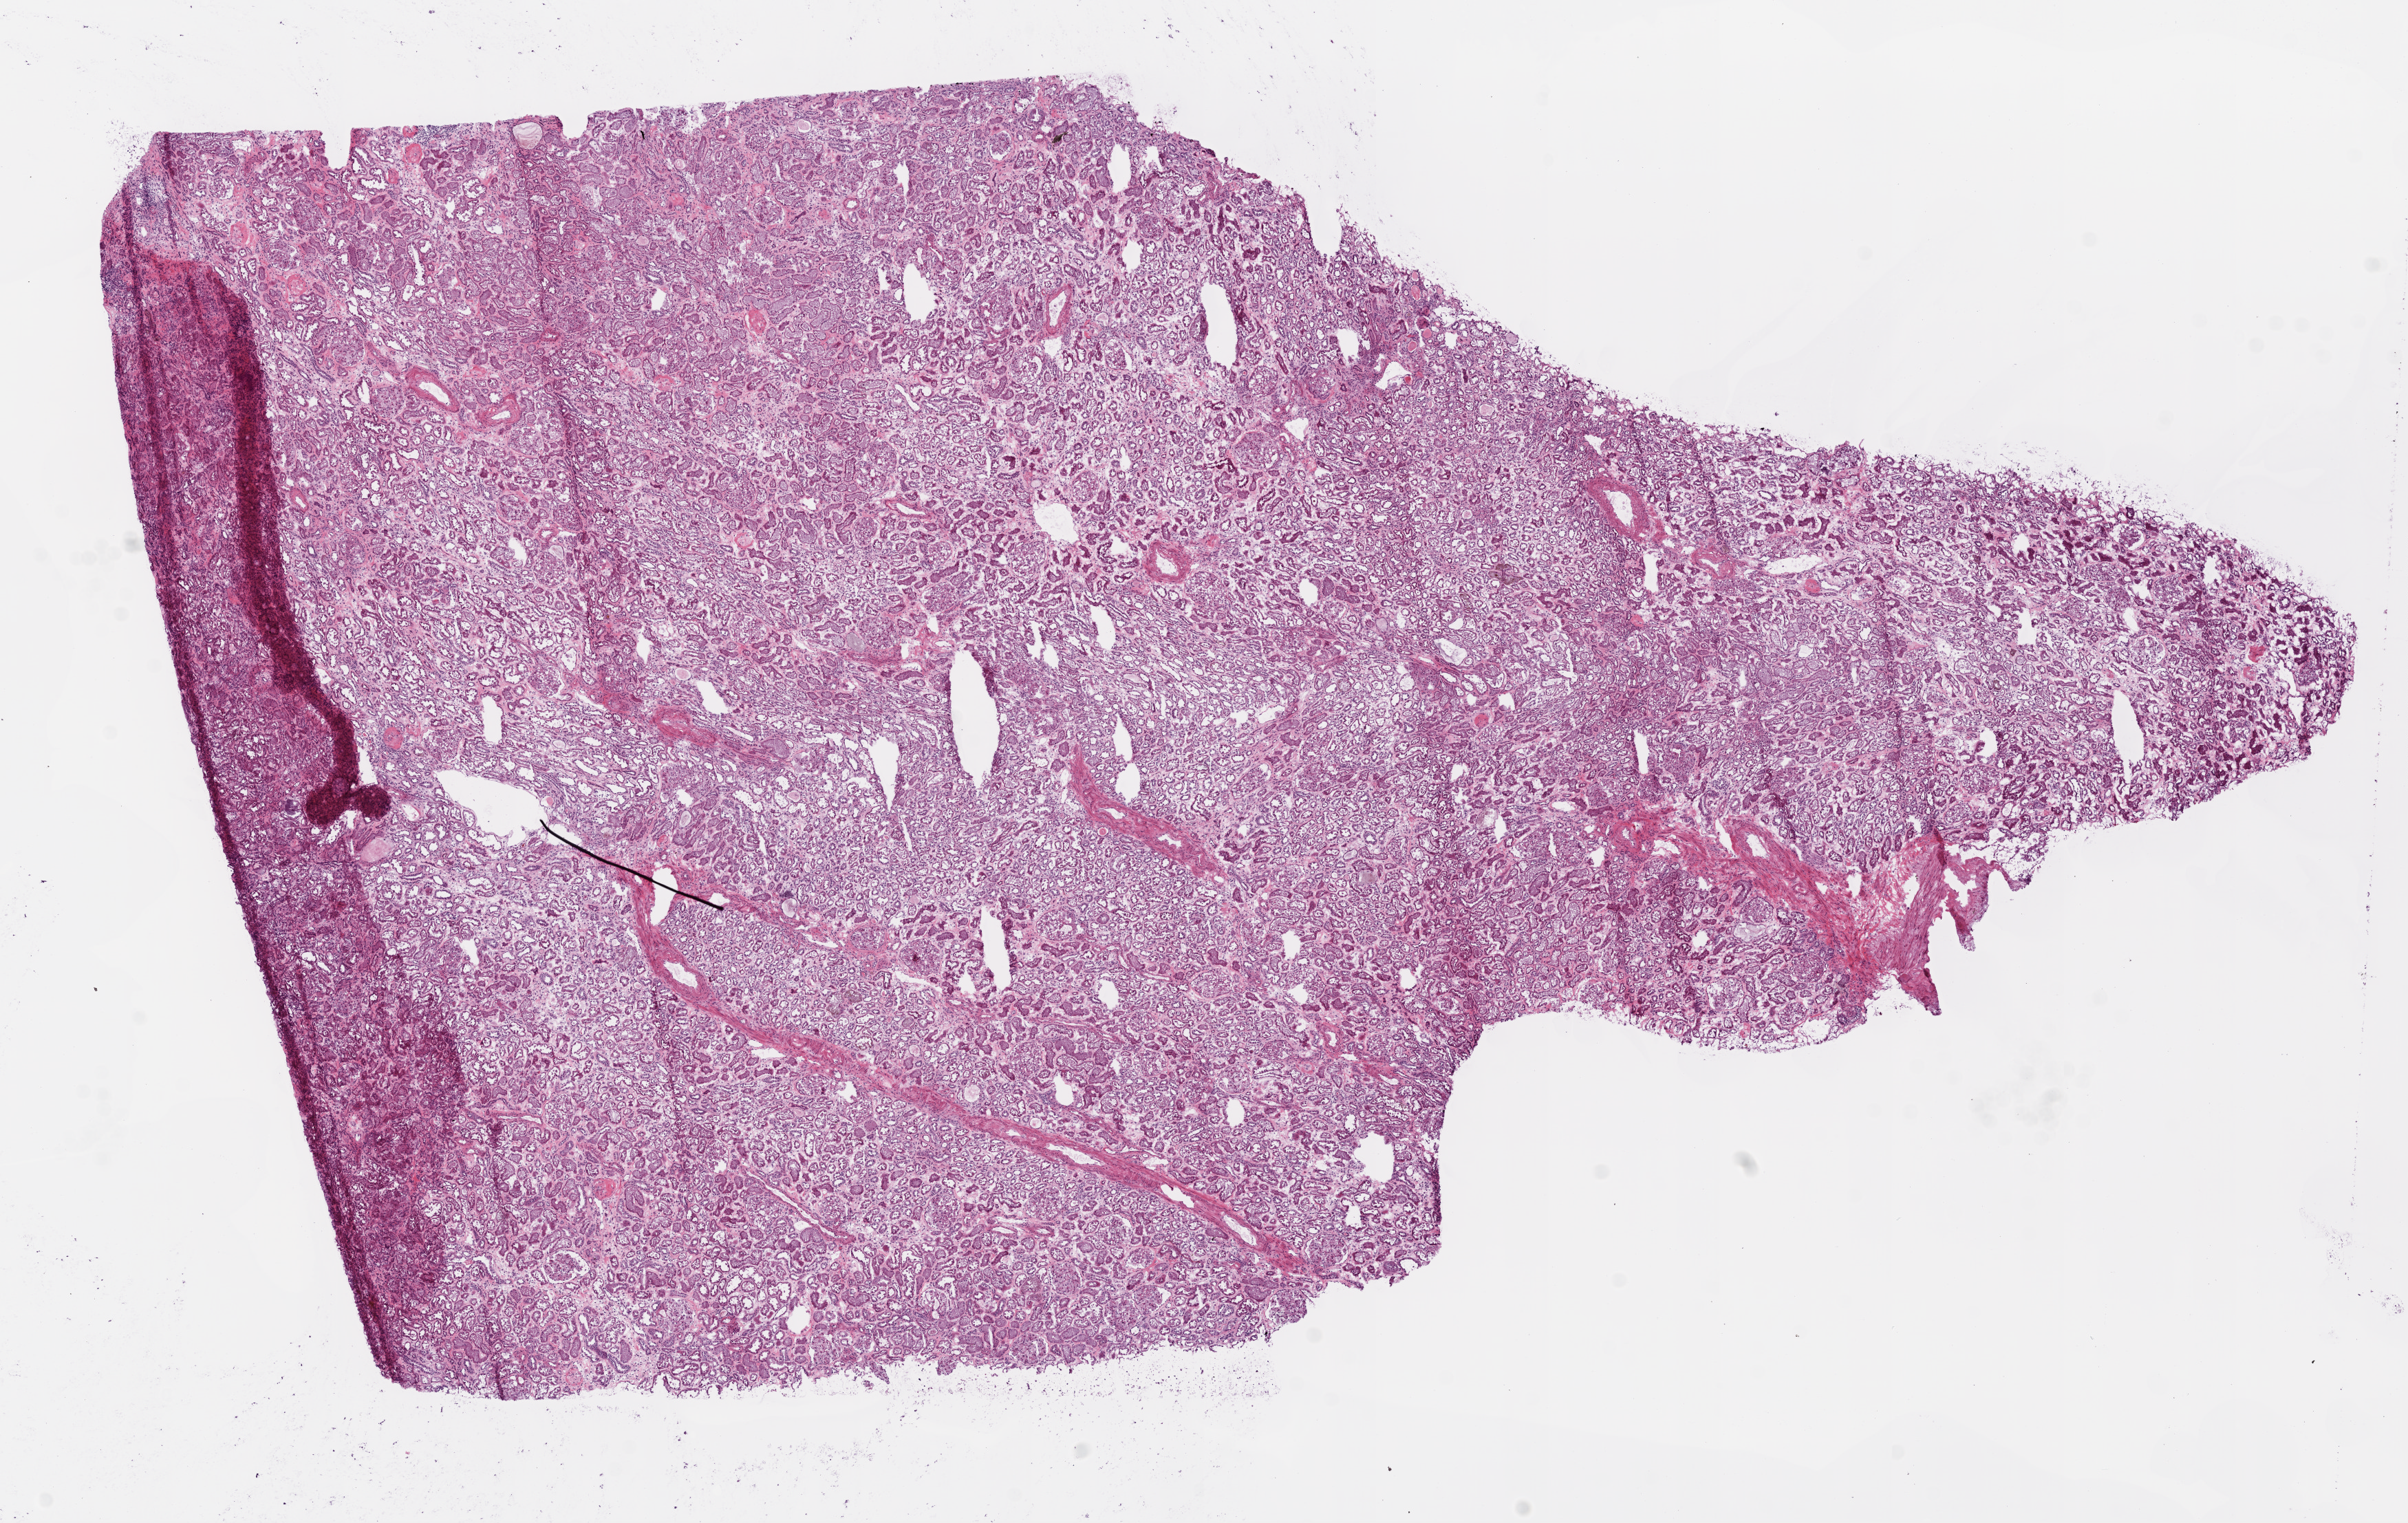
Hematoxylin and eosin (H&E) stained whole-slide image, whole scanned area (about 14.0 x 8.9 mm) shown as a low-resolution overview. Frozen section from the top of the tissue portion. Sample: solid tissue normal (non-tumour tissue), kidney. Male patient; age at initial diagnosis 83 years.
This section: solid tissue normal (non-tumour) sample from the same patient. Patient diagnosis: Clear cell adenocarcinoma, NOS.